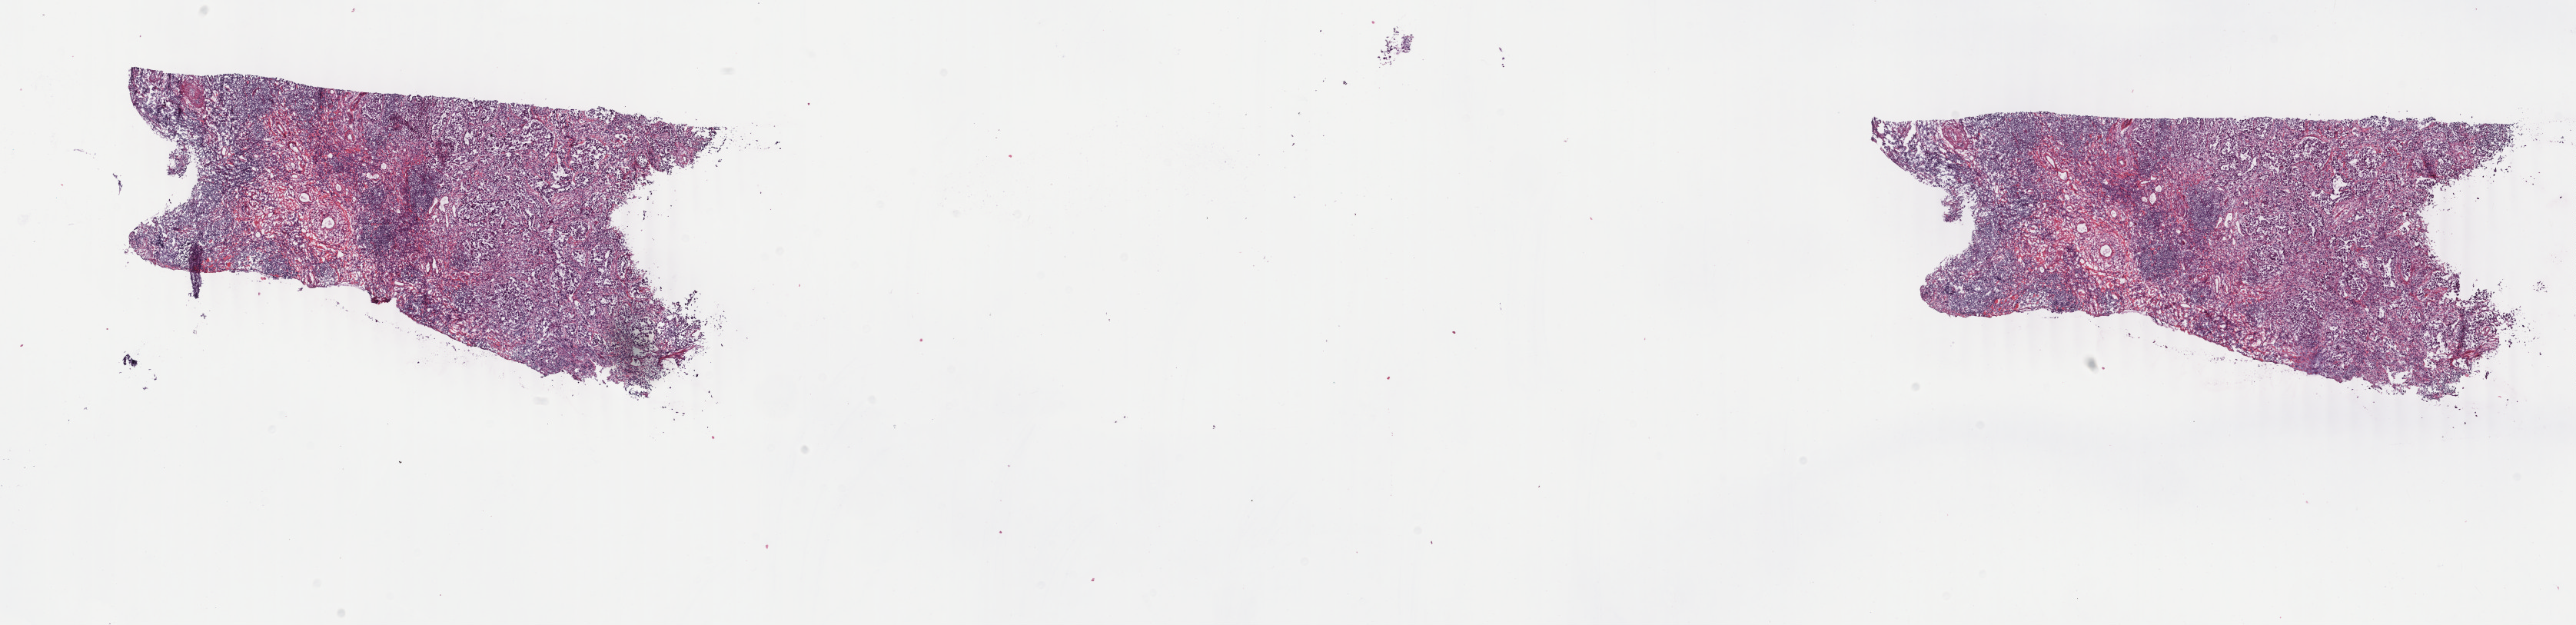
Whole-slide histology image, H&E — a low-resolution overview of the entire scanned area, about 26.7 x 6.5 mm (acquisition: 40x scan); frozen section; primary tumour sample from the lung. Male, age 70 years at initial diagnosis. Composition of this section per pathologist review: tumour cells 60%, tumour nuclei 60%, normal cells 0%, stromal cells 40%, necrosis 0%. Infiltration values recorded for this section: lymphocyte infiltration 10%, monocyte infiltration 2%, neutrophil infiltration 2%.
TNM: T1a N0 MX. AJCC pathologic stage: IA. Pathologic diagnosis: Adenocarcinoma with mixed subtypes (lower lobe, lung). Laterality: right.